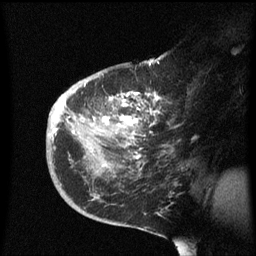
Breast MRI (dynamic contrast-enhanced), one sagittal slice. Position 36 of 60 along the scan axis. Dynamic contrast-enhanced series, image 2 of 3 at this slice position (ordered by acquisition). 1.5 T. TE 4.2 ms, TR 8.4 ms. 2.3 mm slice thickness. 256 × 256 image matrix, field of view 200 × 200 mm. Female patient, age 38 years. Case-level facts recorded for this patient, not image findings: setting: breast cancer imaged before/during neoadjuvant chemotherapy; receptor status: HER2-positive.
Outlined on this slice (semi-automatically segmented with operator editing):
- analysis volume of interest (the breast-tissue region the enhancement analysis was run in; not a lesion): bounding box (x1, y1, x2, y2) in pixels: (46, 78, 190, 213)
- tumour enhancement mask (voxels above the 70 % enhancement threshold inside the analysis volume of interest): (54, 92, 158, 159)